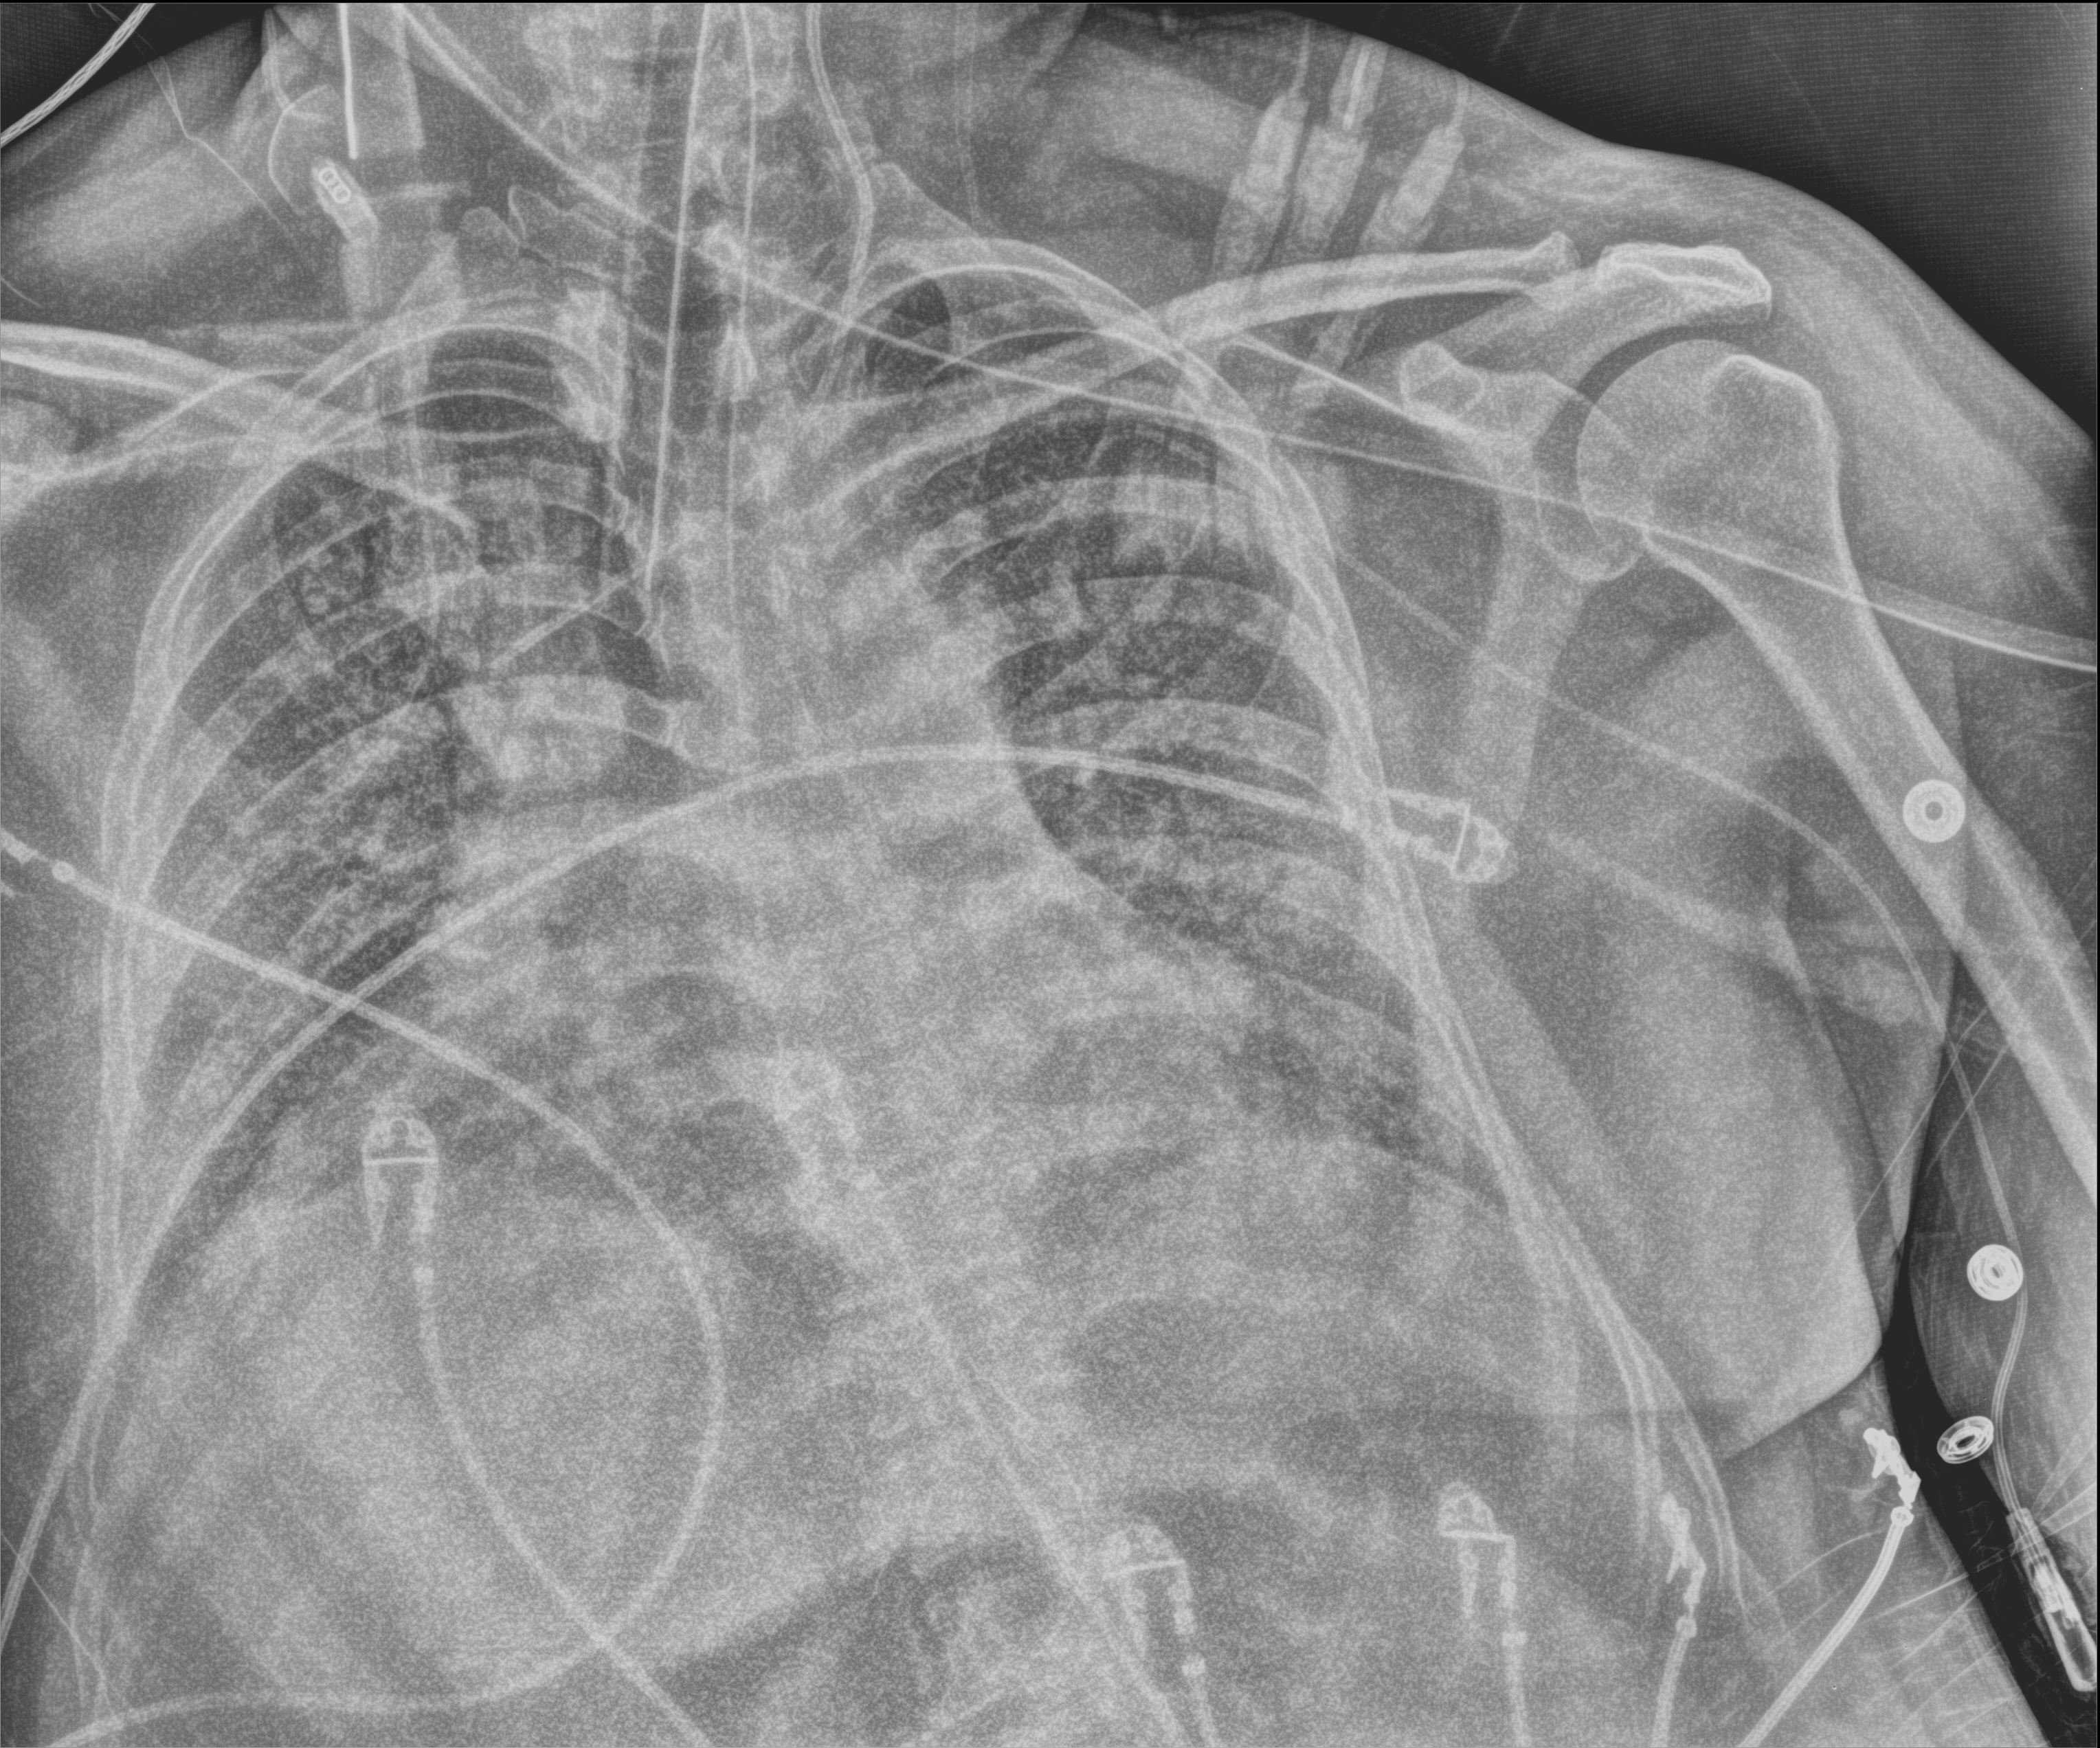
Chest X-ray (portable), anteroposterior (AP) projection. Patient hospitalised with COVID-19, aged 18–59 years.
Hospital-stay facts (about this admission, not read from this image; timing relative to this image not recorded): mechanically ventilated during this hospital stay: yes.